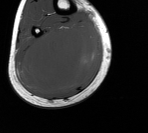
MRI of an extremity soft-tissue mass, one axial slice; position 54 of 76 along the scan axis; MR volume resampled by the dataset authors to the PET/CT grid (not the native acquisition matrix); 3.27 mm slice thickness; 148 × 133 image matrix. Male patient. From the clinical record (not read from this slice): histological type: liposarcoma - round cell; grade: high; site of the primary tumour: right calf.
Outlined on this slice (expert contour drawn on MRI and transferred to this co-registered scan by the dataset authors):
- gross tumour volume (mass): bounding box (x1, y1, x2, y2) in pixels: (17, 21, 101, 95)